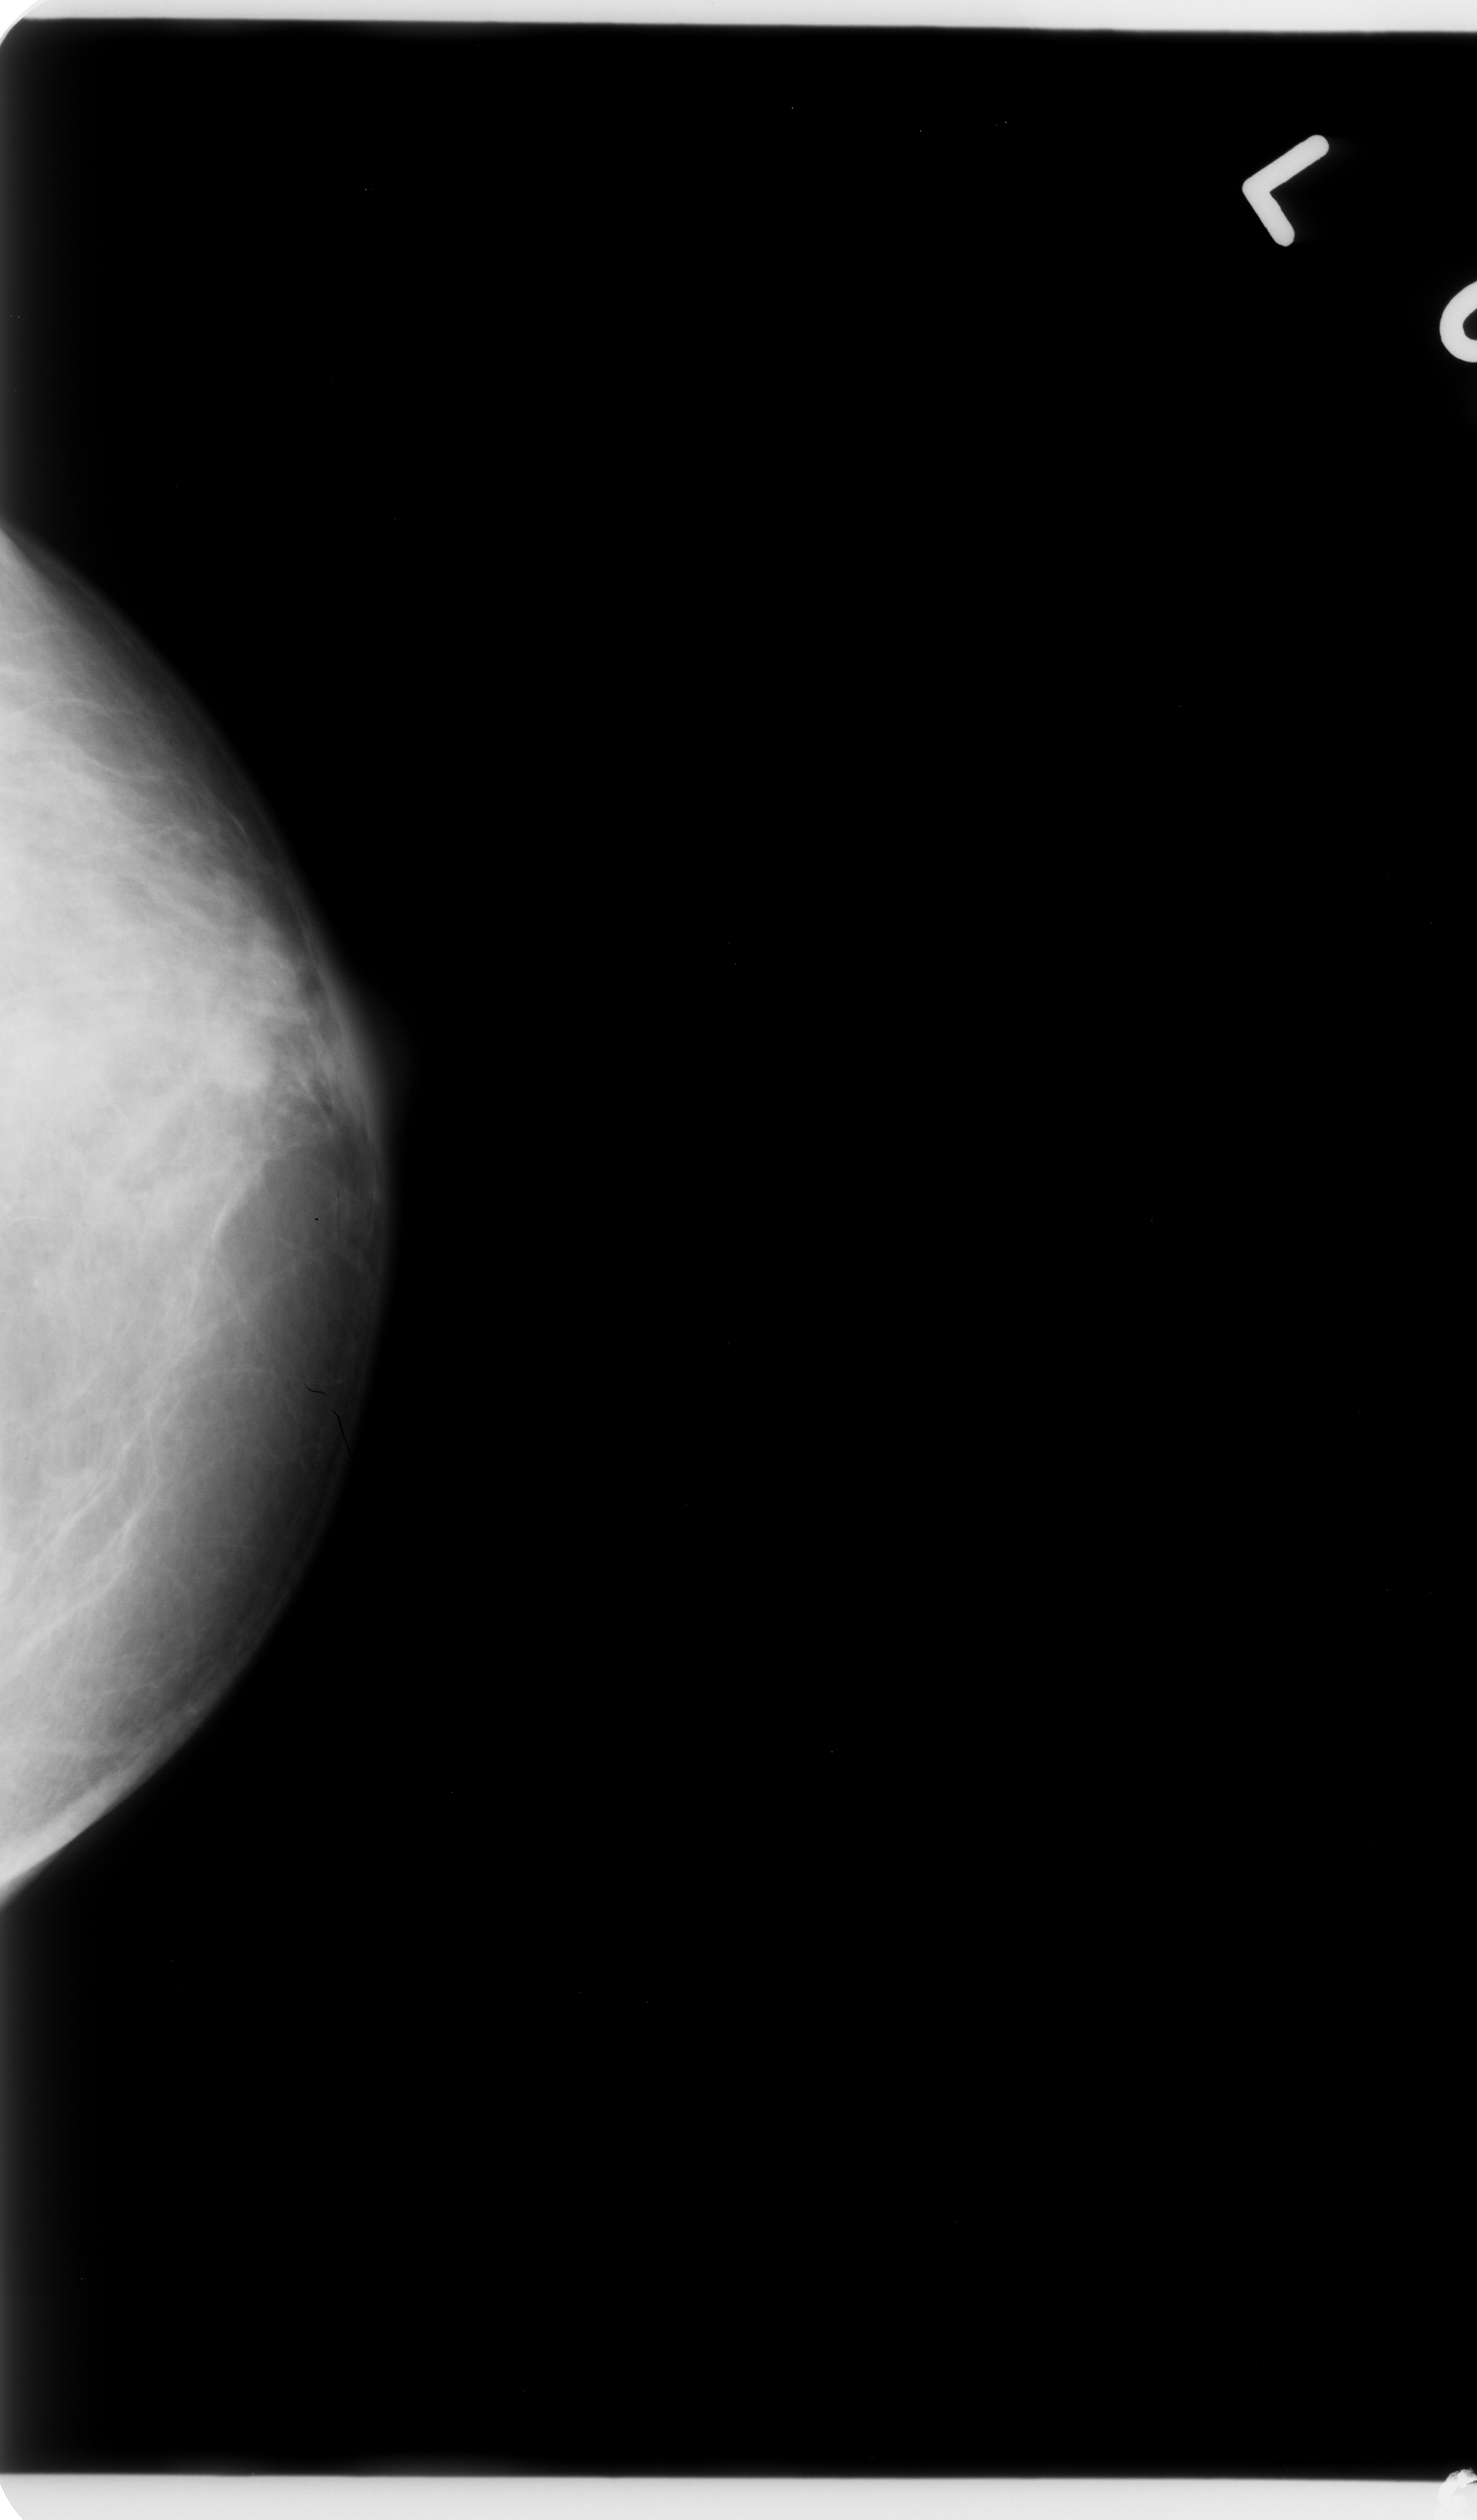
Mammogram (digitized film), left breast, CC view.
Marked abnormality: mass, shape round, margins circumscribed; BI-RADS assessment category 4; pathology (as recorded): benign.